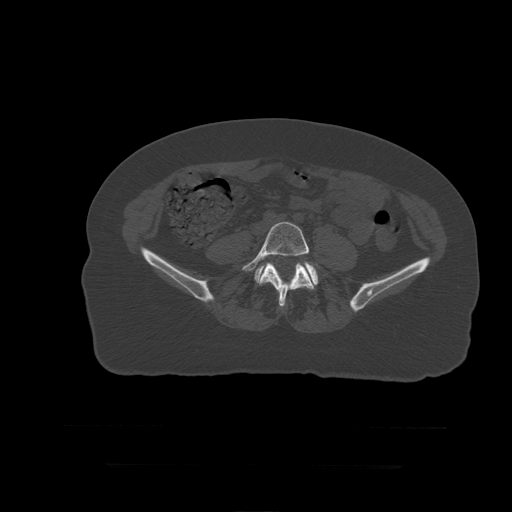
CT including the spine, one axial slice; slice 71 of 399 in the series (ordered by position); reconstruction kernel STANDARD; bone window (W 1800 / L 400 HU); 1.25 mm slice thickness; 512 × 512 image matrix. Patient age 41 years. Case-level facts recorded for this patient, not image findings: primary cancer: breast.
Outlined on this slice (semi-automatic segmentation, software-assisted and operator-edited):
- L5 vertebra: bounding box (x1, y1, x2, y2) in pixels: (242, 223, 318, 307)